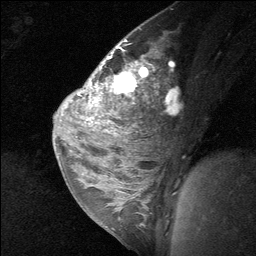
Breast MRI (dynamic contrast-enhanced), one sagittal slice. Slice 41 of 64 in the series (ordered by position). Dynamic contrast-enhanced study with each time point stored as its own series, time point 2 of 3 at this slice position (early post-contrast, ordered by acquisition time). 1.5 T. TE 4.8 ms, TR 27 ms. 256 × 256 image matrix, field of view 180 × 180 mm. Female patient, age 26 years. From the clinical record (not read from this slice): setting: breast cancer imaged before/during neoadjuvant chemotherapy; receptor status: HR-positive, HER2-negative.
Outlined on this slice (semi-automatic segmentation, software-assisted and operator-edited):
- analysis volume of interest (the breast-tissue region the enhancement analysis was run in; not a lesion): bounding box (x1, y1, x2, y2) in pixels: (86, 43, 157, 138)
- tumour enhancement mask (voxels above the 90 % enhancement threshold inside the analysis volume of interest): (88, 57, 147, 120)